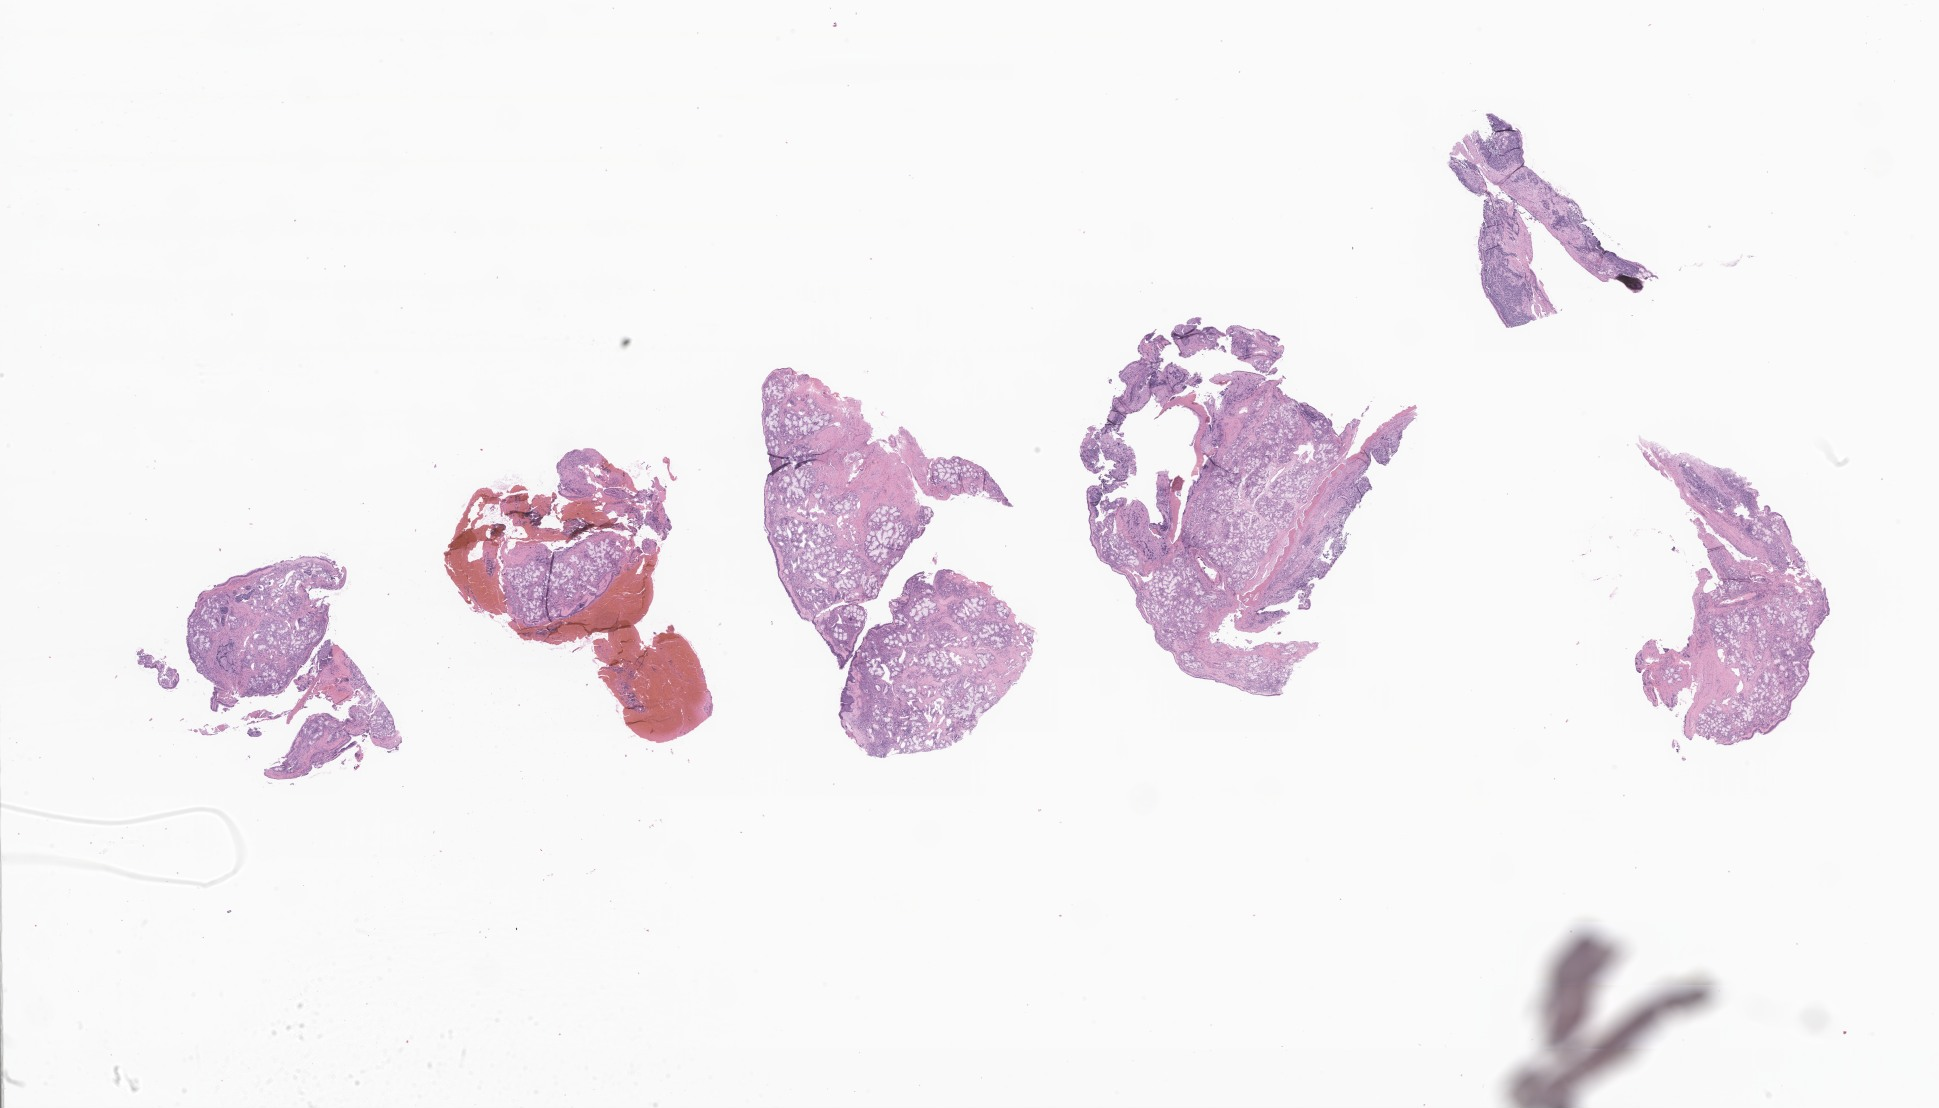
Whole-slide image, hematoxylin and eosin (H&E) stain of tumor tissue from the nasal cavity, whole scanned area (about 32.7 x 18.7 mm) shown as a low-resolution overview; formalin-fixed, paraffin-embedded (FFPE) tissue. Patient: female, age 192 months (16 years).
- diagnosis (ICD-O-3 morphology term): Embryonal rhabdomyosarcoma, NOS